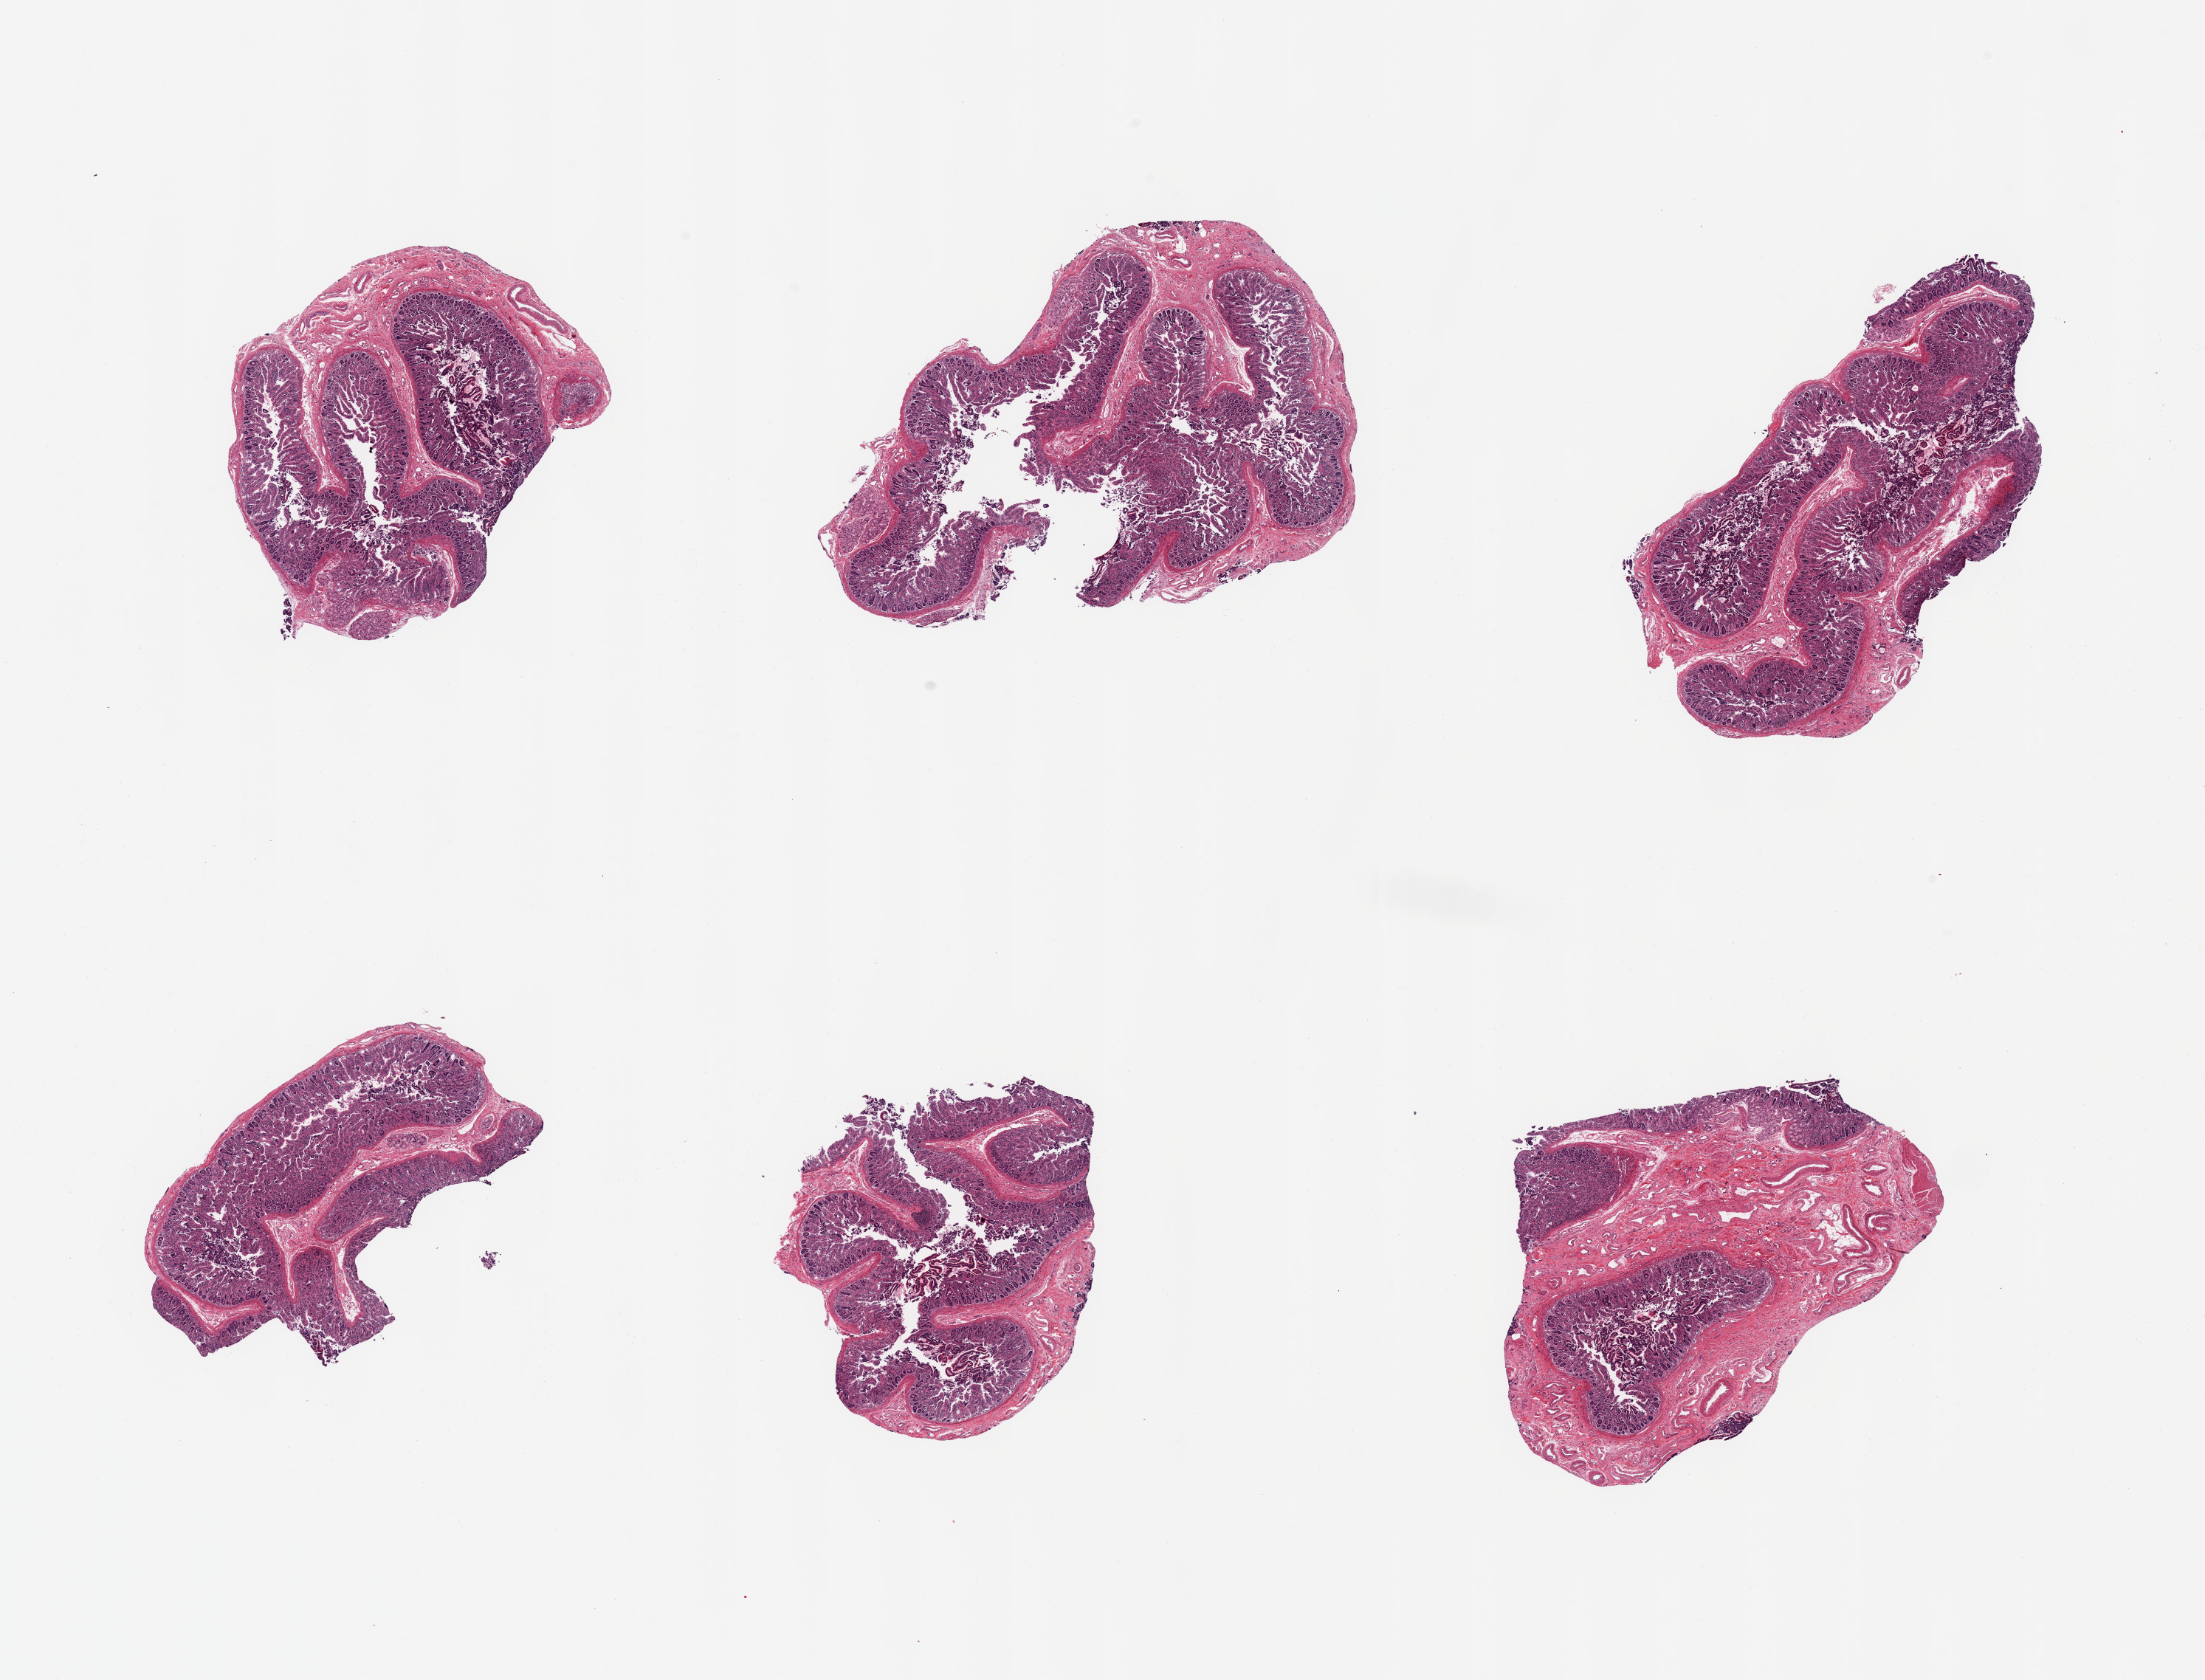
H&E whole-slide image — low-resolution overview of the scanned area, about 23.6 x 18.0 mm, PAXgene-fixed, paraffin-embedded tissue, sampled site (target tissue): ileum, donor tissue sample. Male donor.
• reviewer comment on this tissue sample: 6 pieces; no typical ileum and no lymphoid aggregates; Brunner-type glands; could be distal part of duodenum